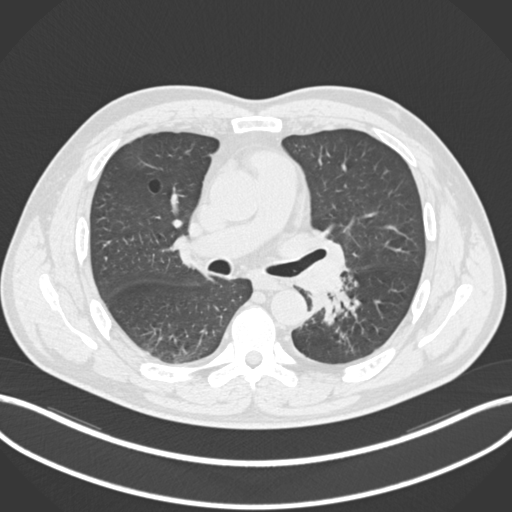
Chest CT, one axial slice. Slice 132 of 223 in the series (ordered by position). 120 kVp. Lung window (W 1500 / L -600 HU). 1 mm slice thickness. 512 × 512 image matrix, field of view 400 × 400 mm. Male patient, age 50 years. Case-level facts recorded for this patient, not image findings: clinical TNM (as recorded): T2a N3 M0.
Structures marked on this image (bounding box drawn by a radiologist):
- lung tumour (recorded histology: squamous cell carcinoma): bounding box (x1, y1, x2, y2) in pixels: (296, 249, 360, 323)